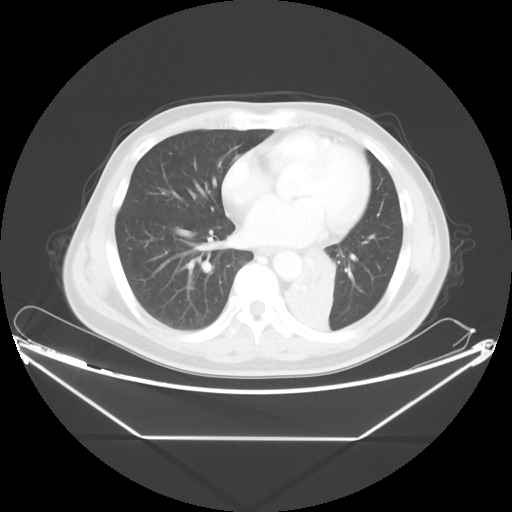
Chest CT, one axial slice; position 19 of 48 along the scan axis; reconstruction kernel STANDARD; 120 kVp; lung window (W 1500 / L -600 HU); 5 mm slice thickness; 512 × 512 image matrix, field of view 438 × 438 mm. Male patient, age 58 years. Case-level facts recorded for this patient, not image findings: clinical TNM (as recorded): T3 N3 M0.
Outlined on this slice (bounding box drawn by a radiologist):
- lung tumour (recorded histology: squamous cell carcinoma): bounding box [x1, y1, x2, y2] px = [292, 250, 334, 329]